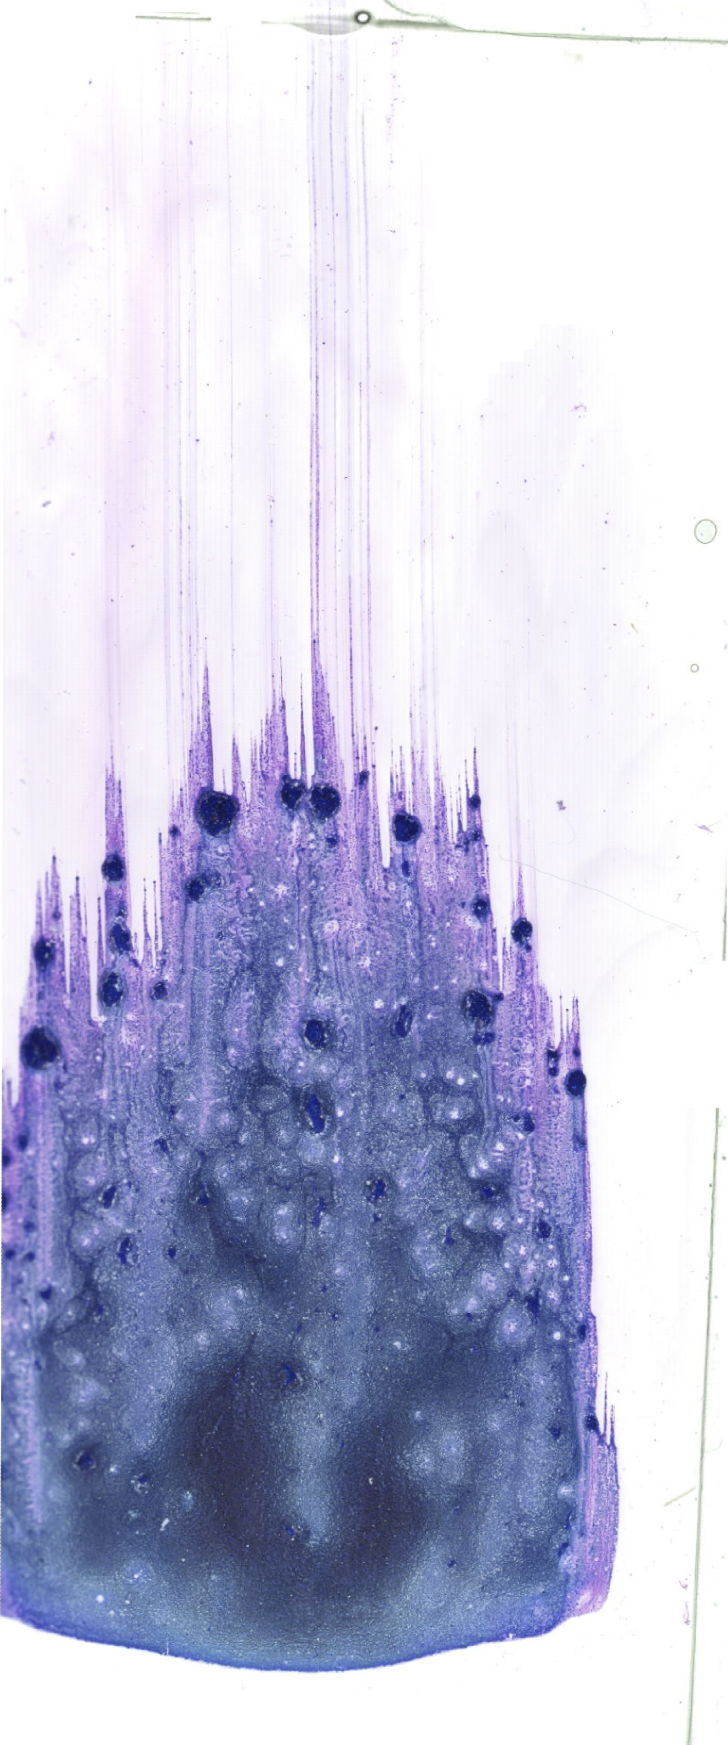
May-Grünwald–Giemsa-stained marrow aspirate smear (whole slide) — a low-resolution overview of the entire scanned area, about 20.6 x 49.5 mm. Female patient.
Diagnosis: Acute Monocytic Leukemia.